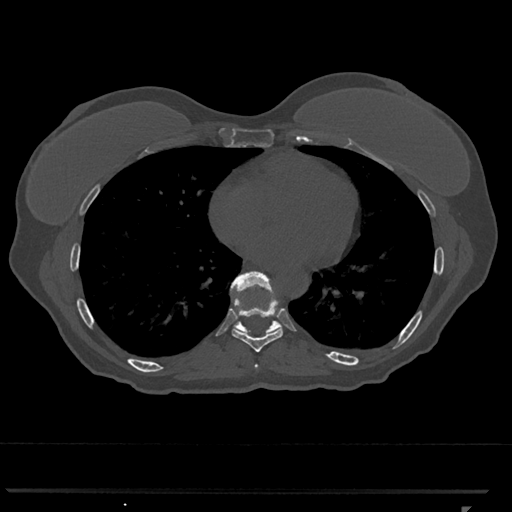
CT including the spine, one axial slice. Position 652 of 793 along the scan axis. Reconstruction kernel Br40s/3. Bone window (W 1800 / L 400 HU). 0.5 mm slice thickness. 512 × 512 image matrix. Patient: female, 62 years. From the clinical record (not read from this slice): primary cancer: renal.
Outlined on this slice (semi-automatically segmented with operator editing):
- T7 vertebra: box from (x=255, y=364) to (x=259, y=368) px
- T8 vertebra: (x=232, y=299)–(x=283, y=352)
- T9 vertebra: (x=230, y=271)–(x=282, y=335)